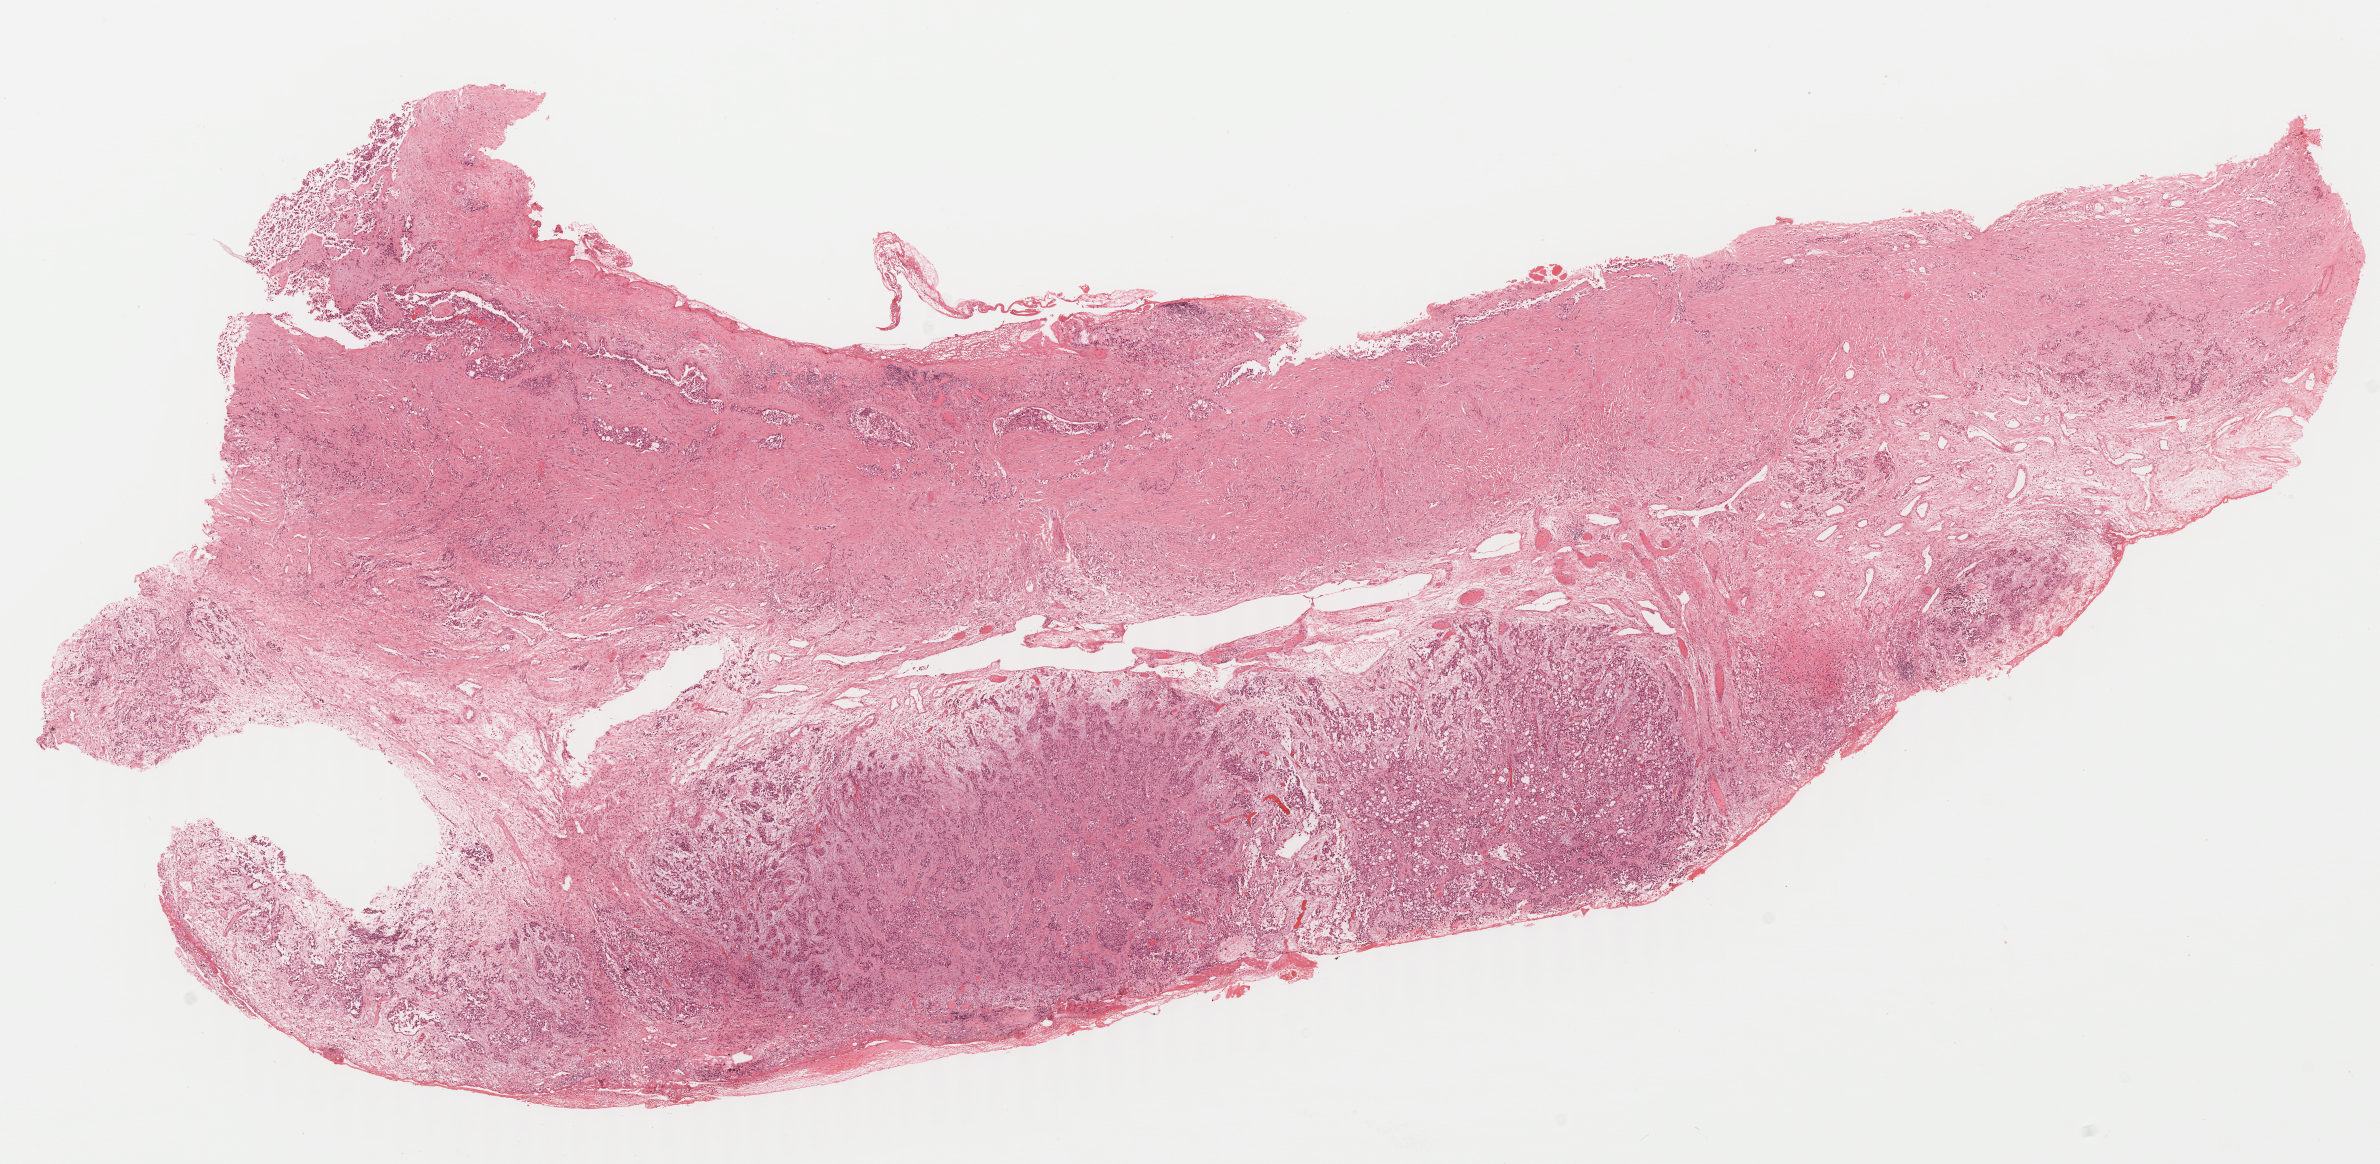
Whole-slide histology image, H&E — whole scanned area (about 18.8 x 9.2 mm, from a 40x scan) shown as a low-resolution overview; FFPE section; sample: primary tumour, mesothelium. Patient: male, age at initial diagnosis 66 years.
Diagnosis: Epithelioid mesothelioma, malignant (pleura, NOS). AJCC pathologic stage: I (6th edition).